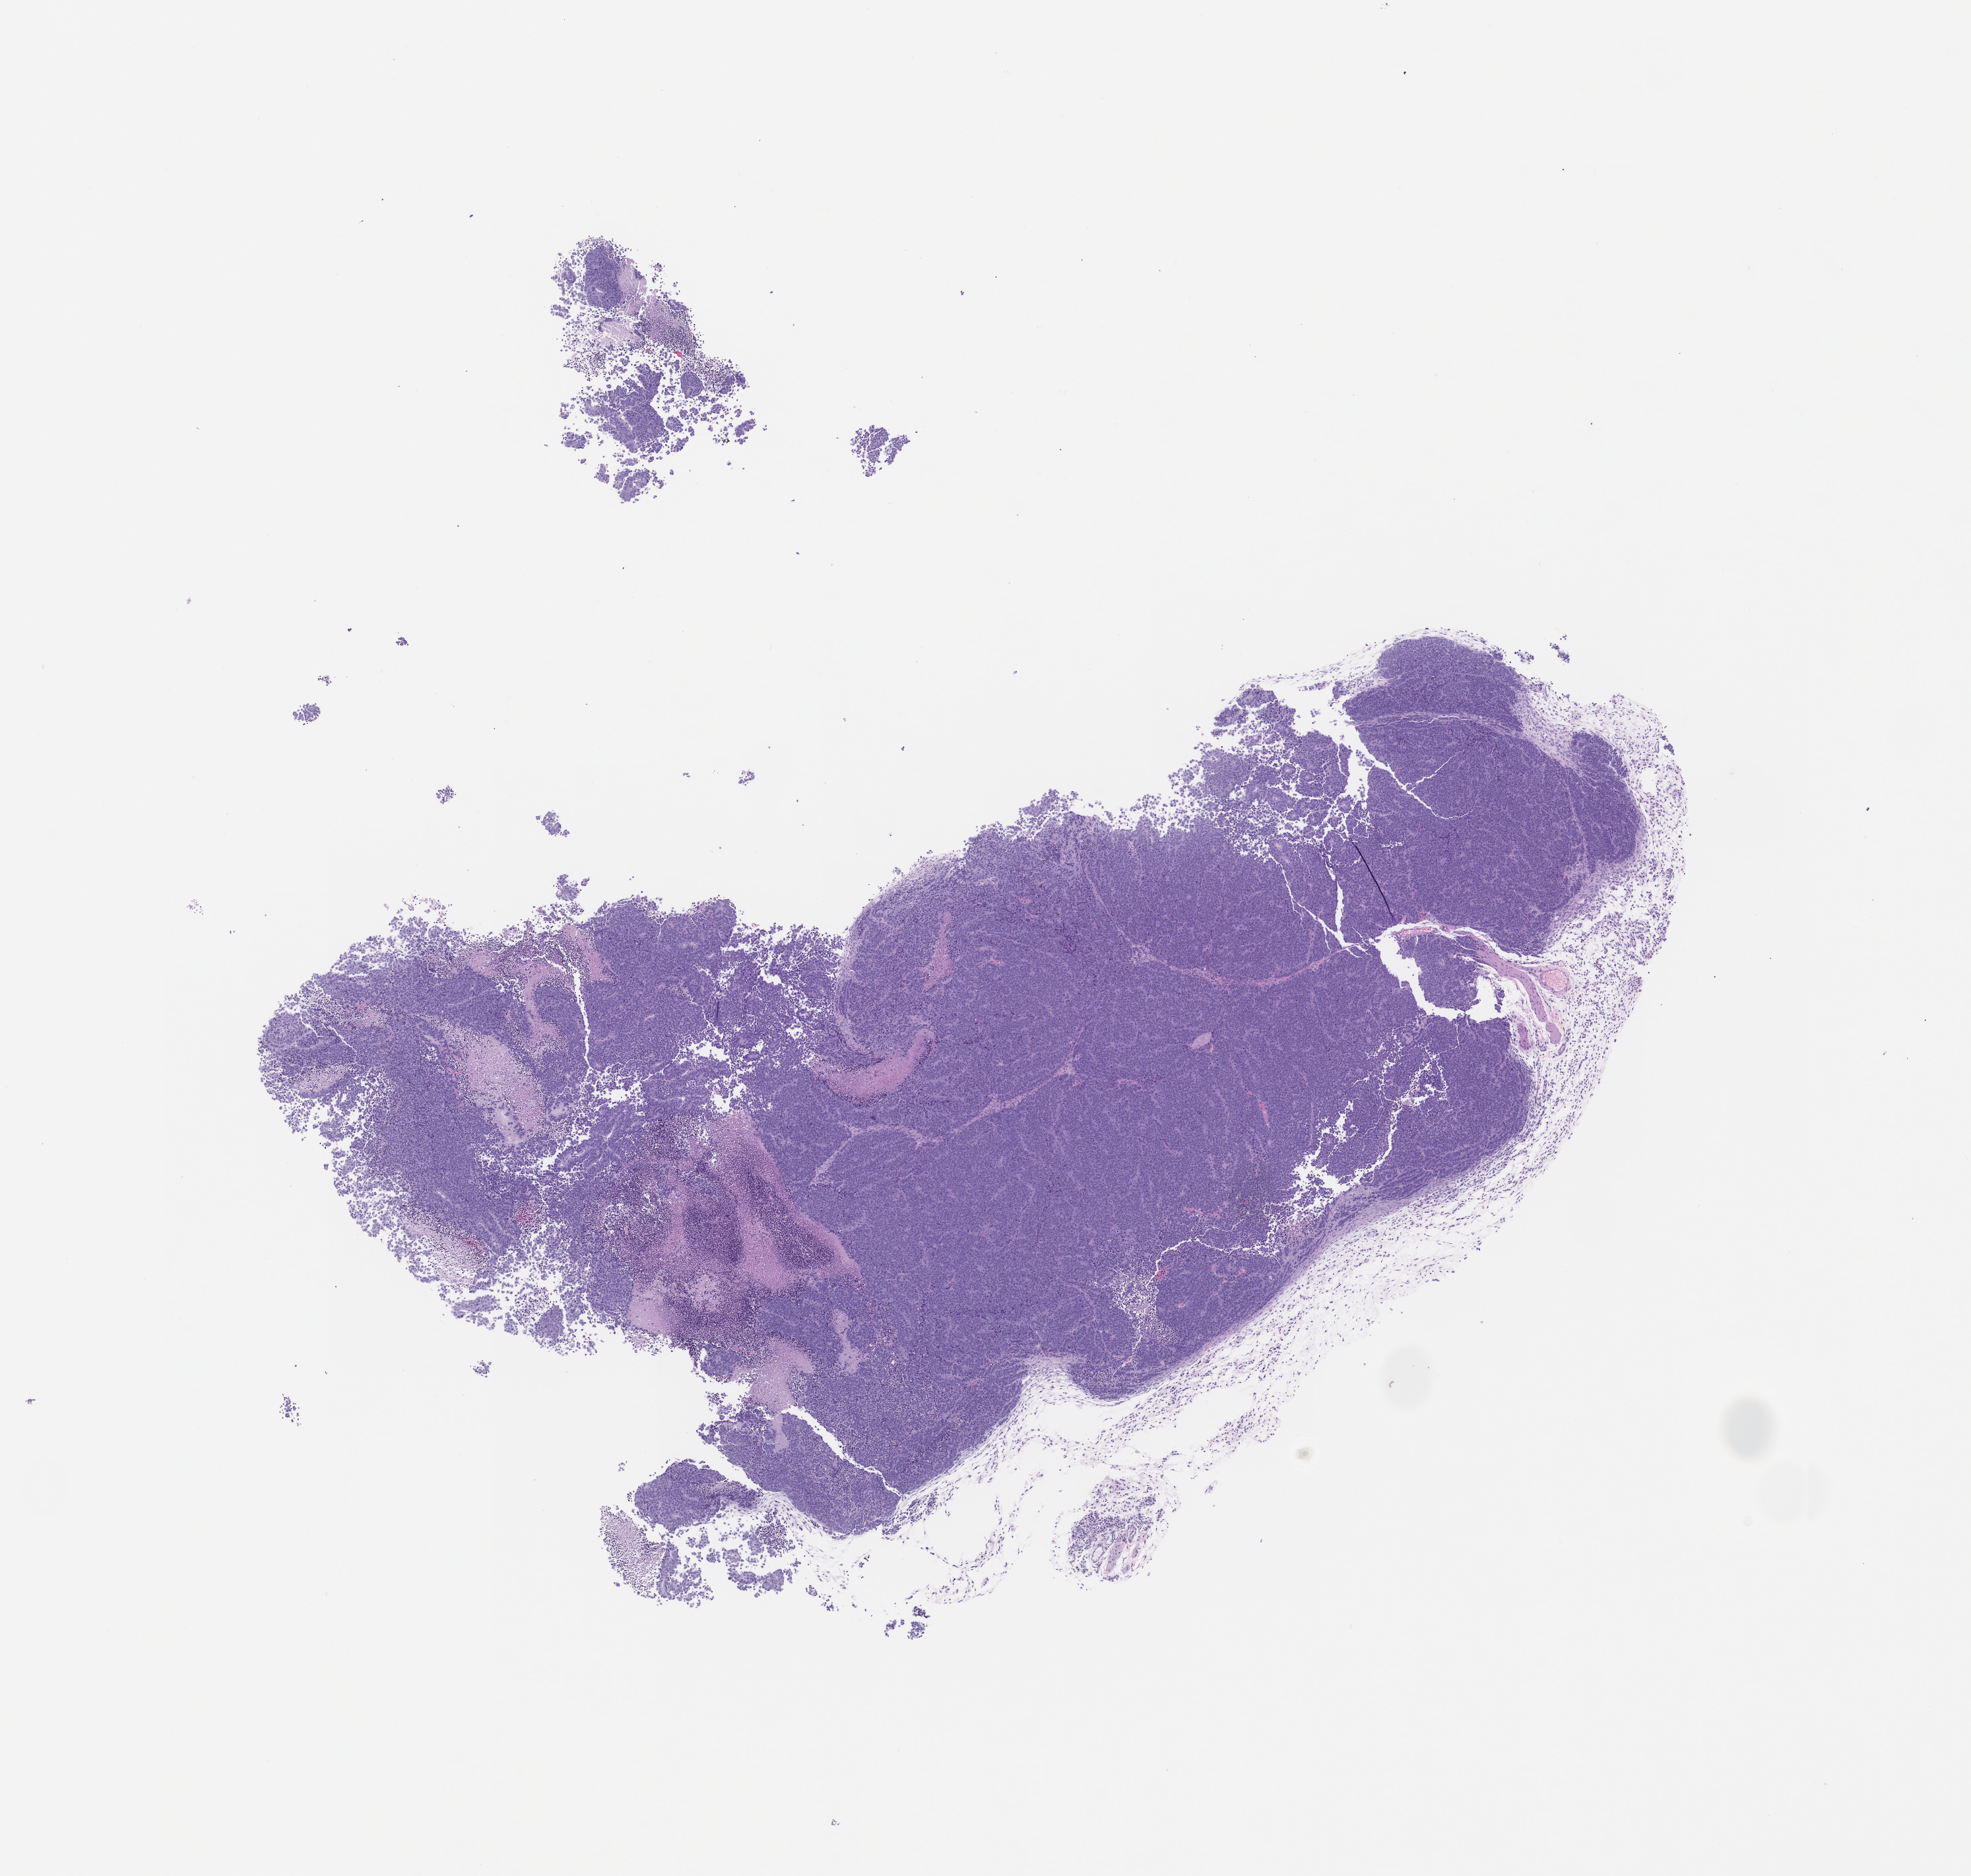
Whole-slide image, hematoxylin and eosin (H&E): patient-derived xenograft (human tumor grown in a mouse), passage 1, a low-resolution overview of the entire scanned area, about 12.0 x 11.4 mm. FFPE section. Originating tumor site category: bladder.
Originating patient diagnosis: Urothelial Carcinoma.